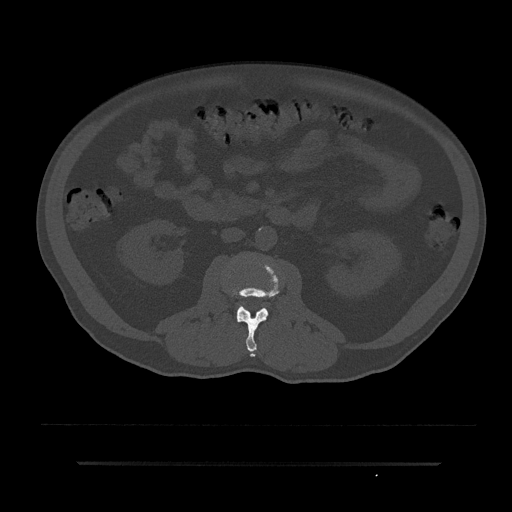
CT including the spine, one axial slice; reconstruction kernel Br40s/3; 120 kVp; bone window (W 1800 / L 400 HU); 0.5 mm slice thickness; 512 × 512 image matrix. Patient: male, 59 years. Case-level facts recorded for this patient, not image findings: primary cancer: bile ducts; vertebrae with lytic lesions (as recorded): T10.
Outlined on this slice (semi-automatically segmented with operator editing):
- L2 vertebra: box from (x=227, y=263) to (x=281, y=357) px